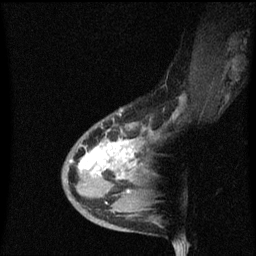
Breast MRI (dynamic contrast-enhanced), one sagittal slice. Position 28 of 60 along the scan axis. Dynamic contrast-enhanced series, image 2 of 3 at this slice position (ordered by acquisition). 1.5 T. TE 4.2 ms, TR 8.4 ms. 256 × 256 image matrix, field of view 200 × 200 mm. Female patient, age 38 years. From the clinical record (not read from this slice): setting: breast cancer imaged before/during neoadjuvant chemotherapy; receptor status: HR-positive, HER2-negative.
Outlined on this slice (semi-automatically segmented with operator editing):
- analysis volume of interest (the breast-tissue region the enhancement analysis was run in; not a lesion): box from (x=62, y=114) to (x=149, y=205) px
- tumour enhancement mask (voxels above the 70 % enhancement threshold inside the analysis volume of interest): (x=78, y=140)–(x=135, y=179)